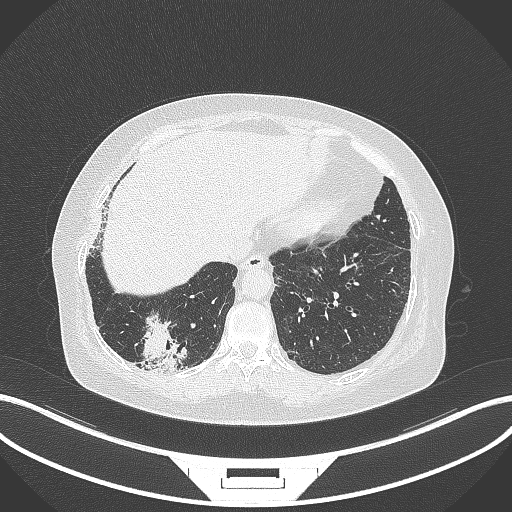
Chest CT, one axial slice. Position 37 of 296 along the scan axis. Lung window (W 1500 / L -600 HU). 1 mm slice thickness. 512 × 512 image matrix, field of view 400 × 400 mm. Female patient, age 65 years. Case-level facts recorded for this patient, not image findings: clinical TNM (as recorded): T2b N1 M0.
Structures marked on this image (rectangle marked by the reading radiologist):
- lung tumour (recorded histology: adenocarcinoma): box from (x=134, y=312) to (x=189, y=374) px